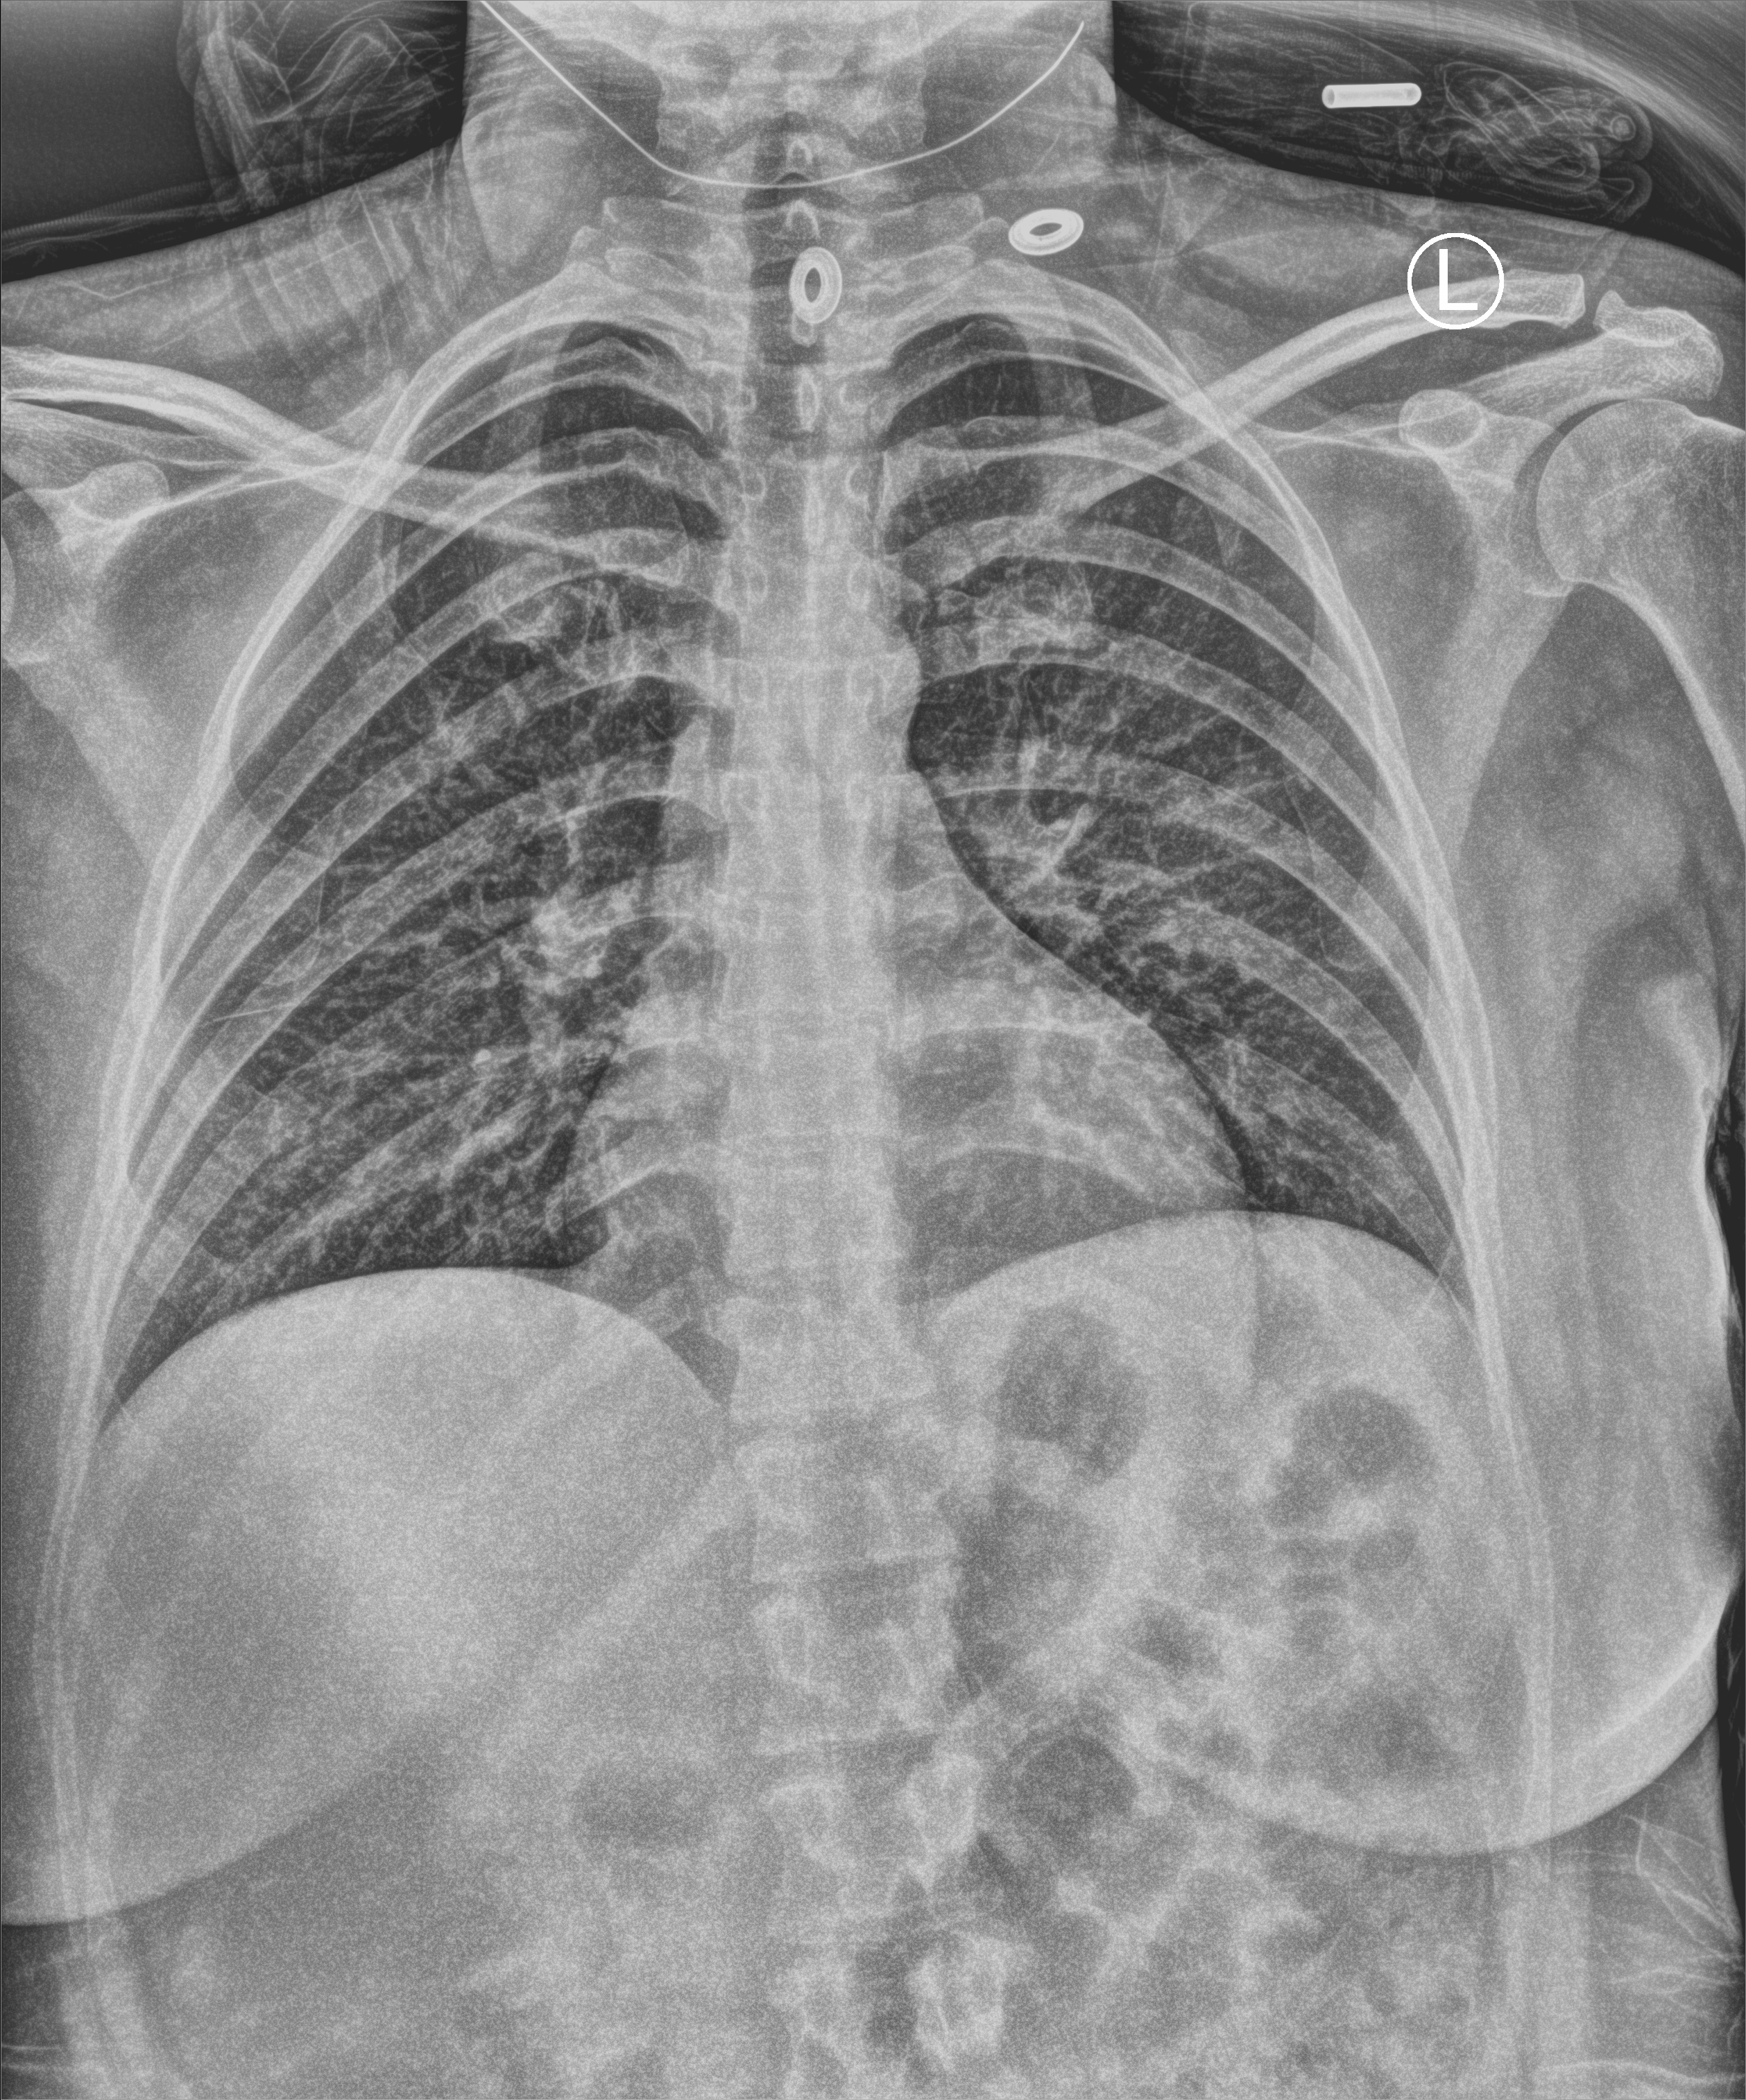
Bedside chest radiograph (computed radiography). Patient hospitalised with COVID-19; female, aged 18–59 years.
From the hospital-stay record, not from the radiograph (when in the stay this image was taken is not recorded): mechanically ventilated during this hospital stay: no; admitted to intensive care during this hospital stay: no; smoking status (admission record): never.